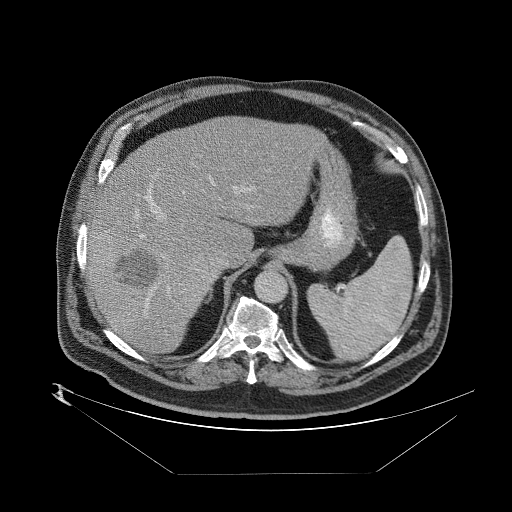
Contrast-enhanced abdominal CT (liver protocol), one axial slice; position 58 of 89 along the scan axis; 140 kVp; one of 2 acquisitions stored at this slice position; soft-tissue window (W 400 / L 40 HU); 512 × 512 image matrix, field of view 480 × 480 mm. Case-level facts recorded for this patient, not image findings: diagnosis: hepatocellular carcinoma (patient treated with transarterial chemoembolisation; whether this scan precedes or follows treatment is not stated here); TNM stage (as recorded): Stage-II; Child-Pugh class: B; tumour differentiation: moderately differentiated; tumour size: 4 cm.
Outlined on this slice (semi-automatically segmented with operator editing):
- abdominal aorta: bounding box [x1, y1, x2, y2] px = [255, 269, 287, 302]
- liver parenchyma outside the tumour (the mass and vessels are separate outlines, so this box may not span the whole liver): [88, 114, 318, 352]
- mass: [88, 233, 229, 309]
- liver vessels: [125, 192, 256, 311]